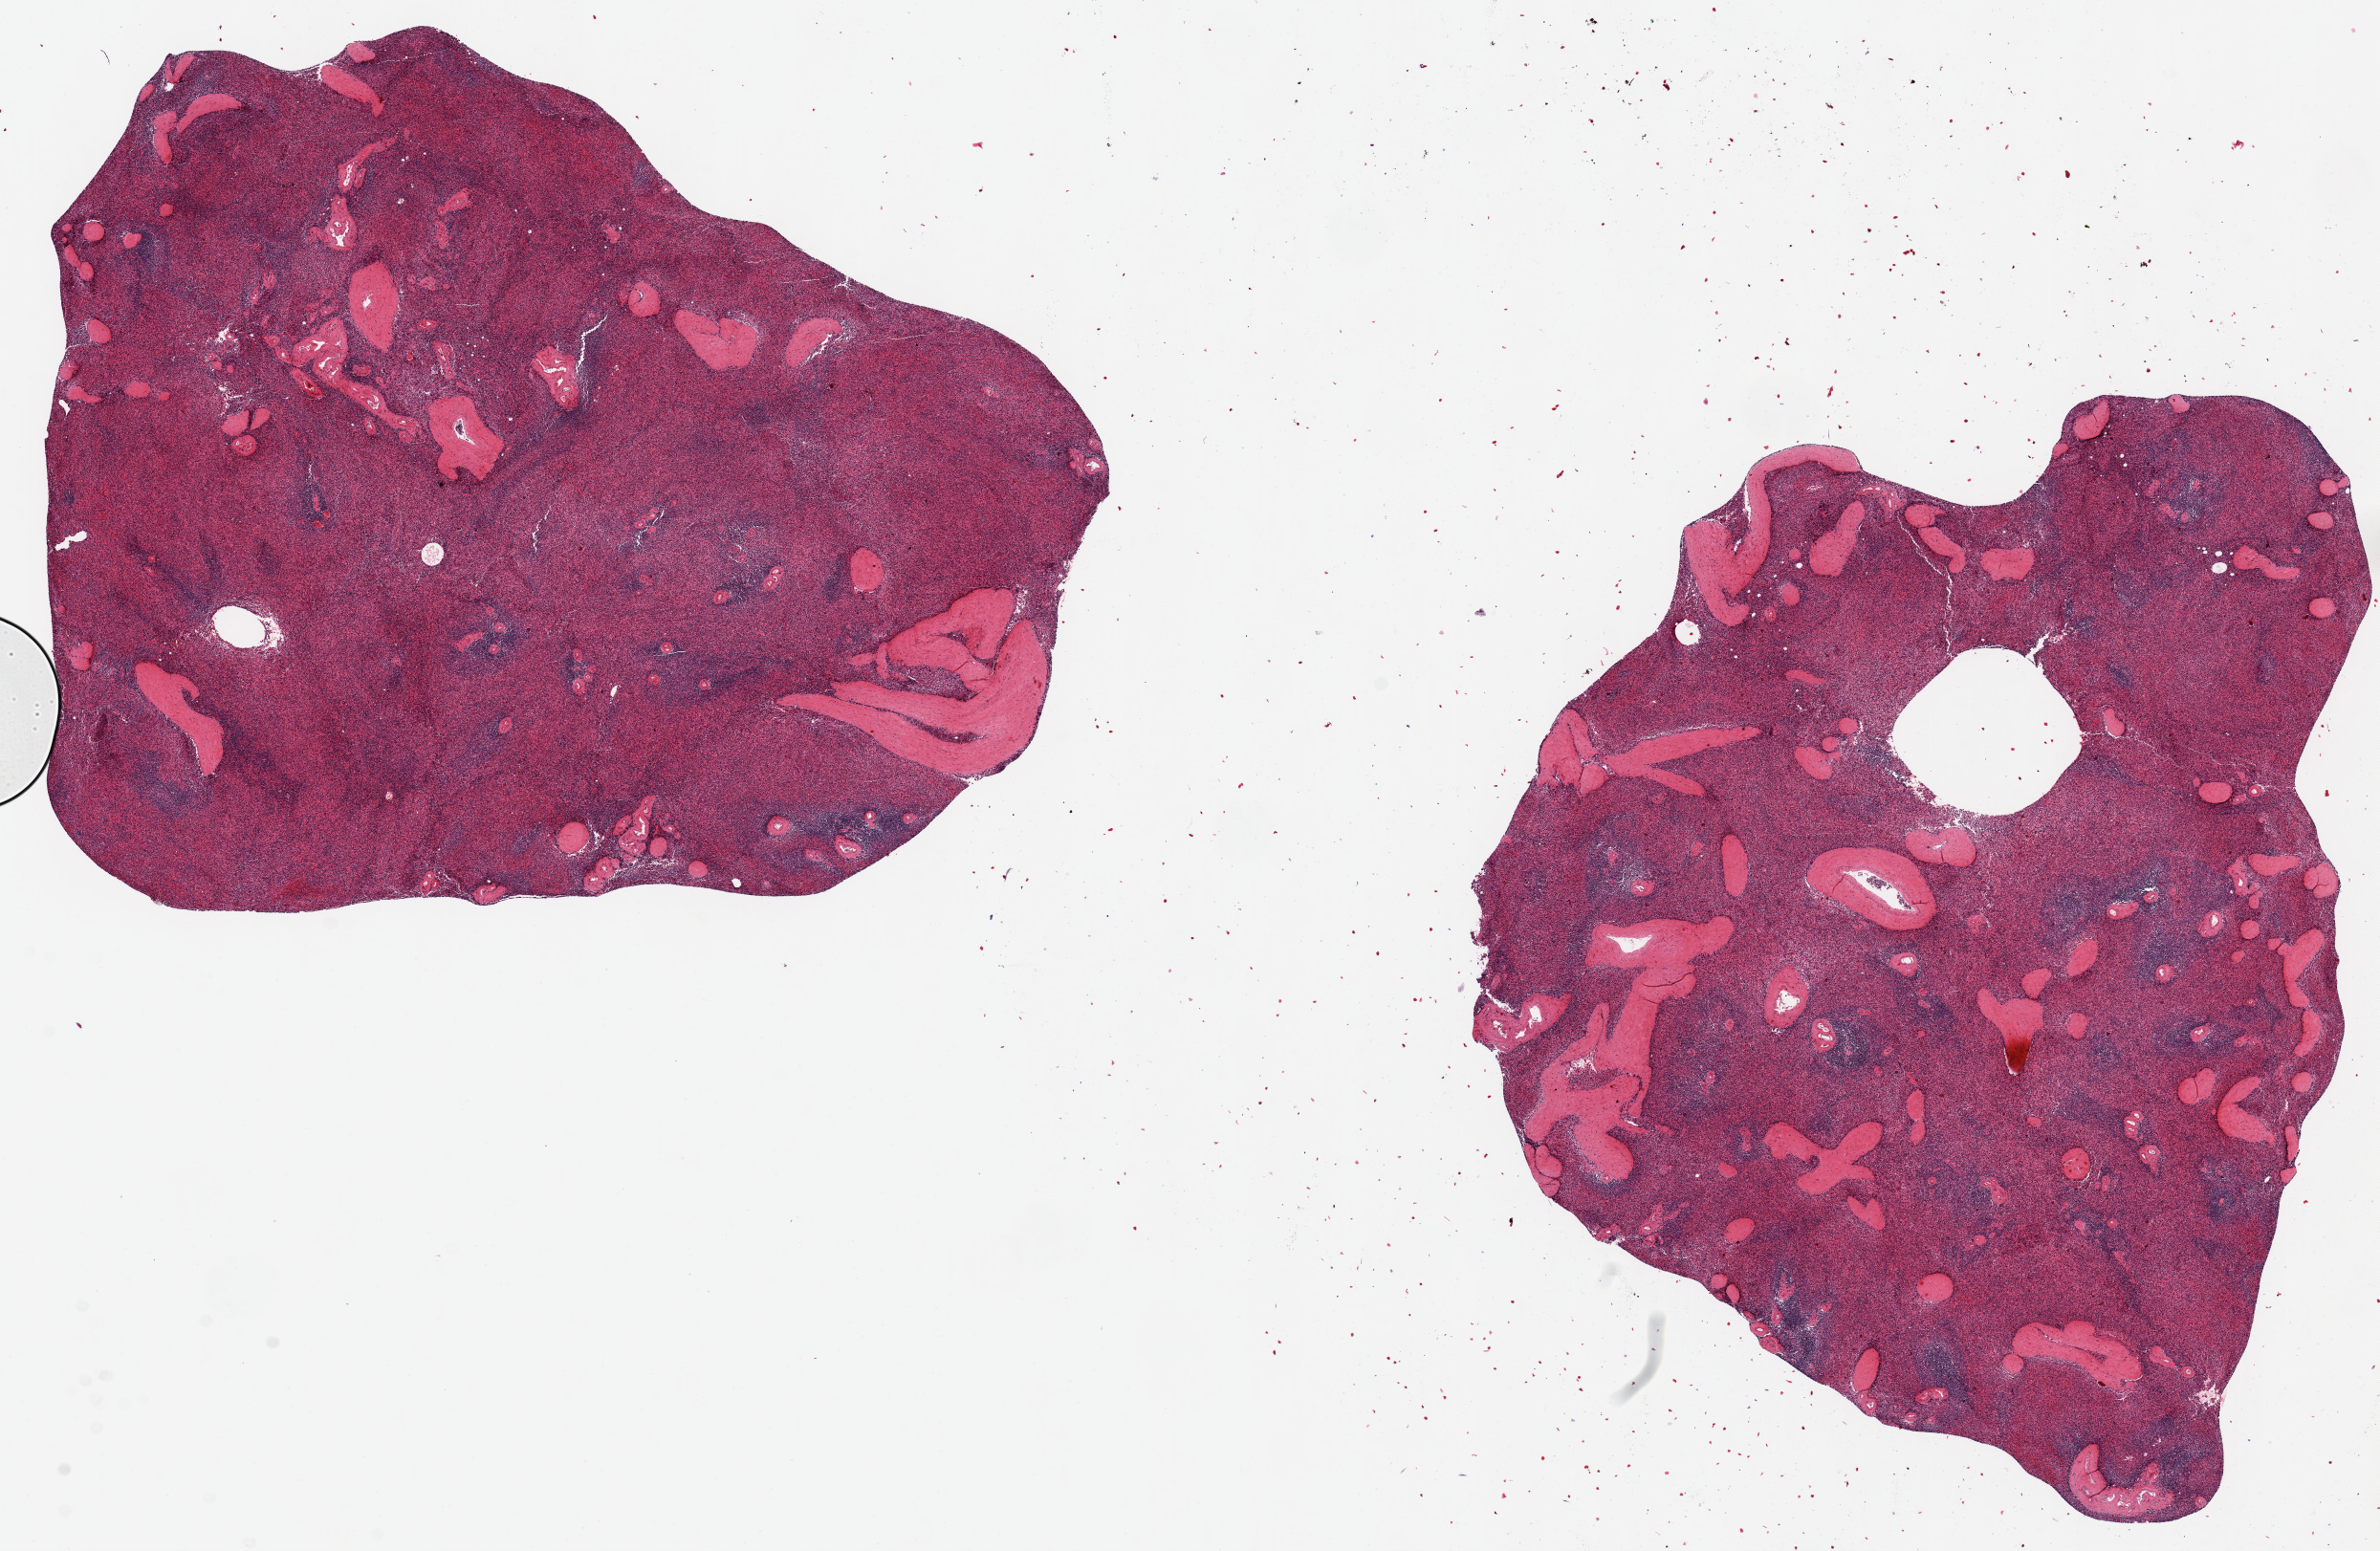
Whole-slide image, H&E stain, brightfield, shown as a low-resolution overview of the whole scanned area (about 19.7 x 12.8 mm, from a 20x scan). PAXgene-fixed, paraffin-embedded tissue. Sampled site (target tissue): spleen. Donor tissue sample. Donor sex: male.
Reviewer comment on this tissue sample: 2 pieces ~8x5mm.